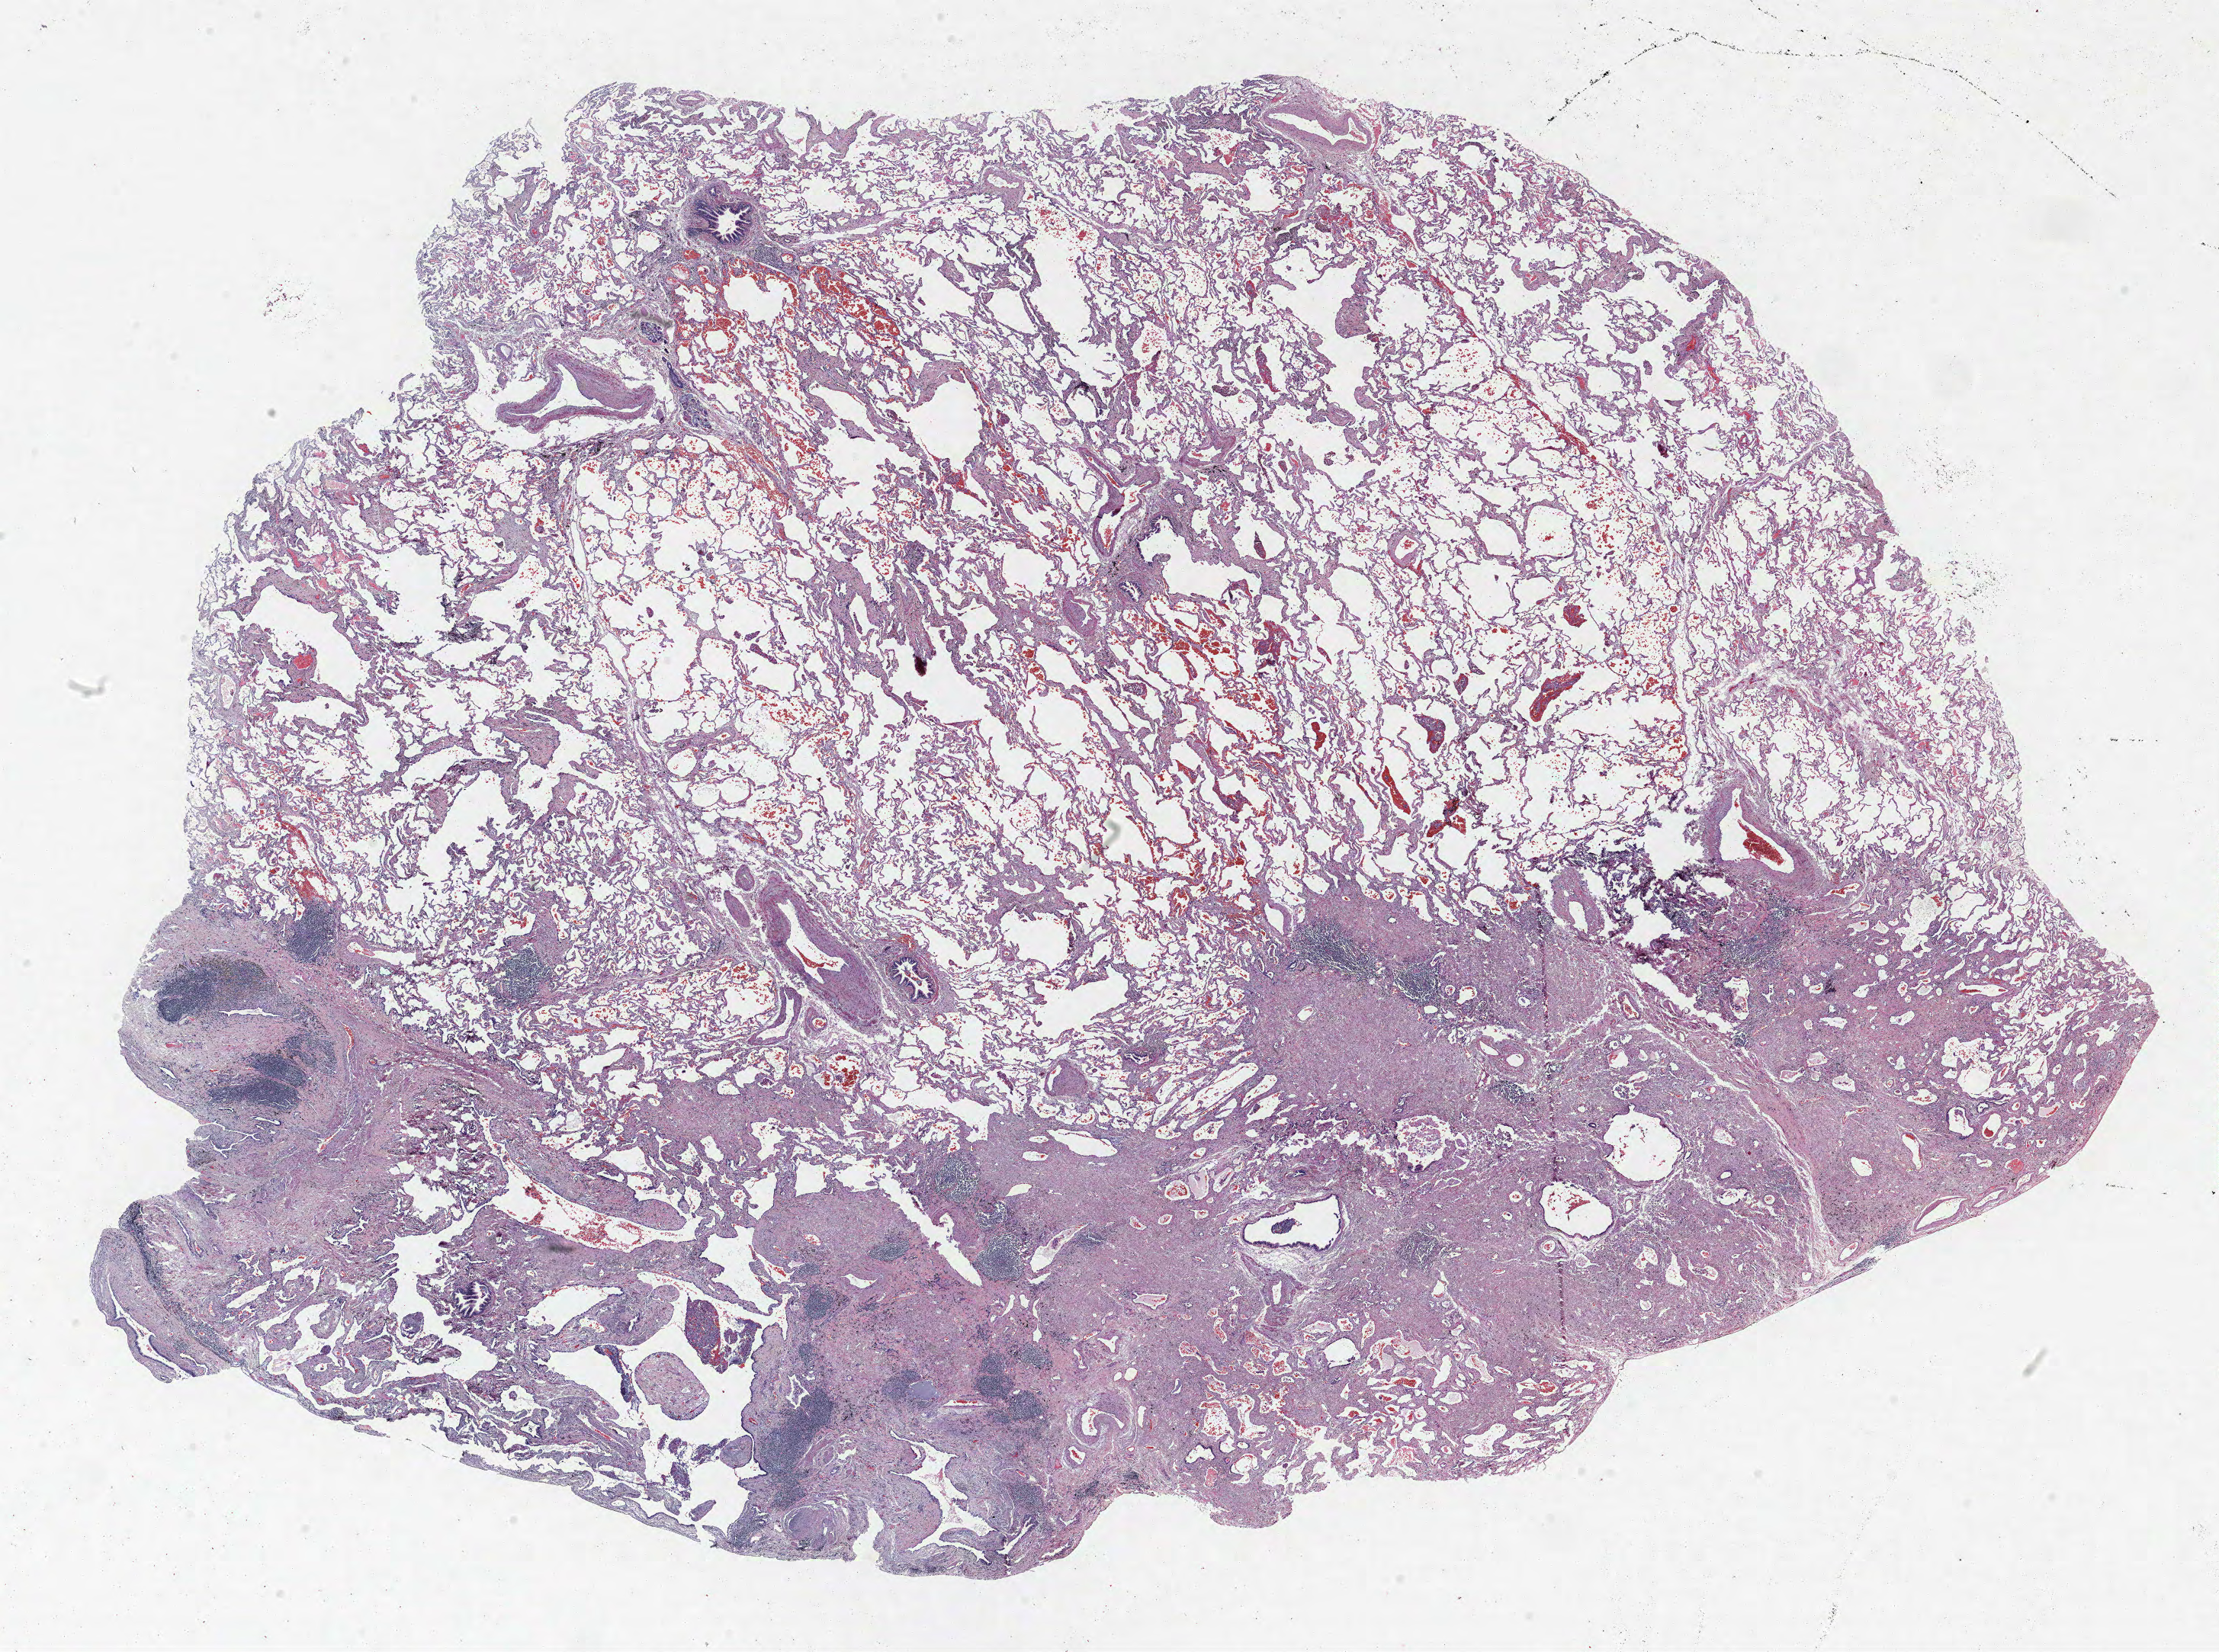
Whole-slide histology image, H&E, whole scanned area (about 23.3 x 17.3 mm) shown as a low-resolution overview; formalin-fixed paraffin-embedded (FFPE) section; lung tissue. Female, age 66 at enrolment. Current smoker at enrolment. Grade: poorly differentiated (G3).
* participant's lung-cancer diagnosis: Adenocarcinoma, NOS (ICD-O-3 8140/3)
* tumour size (pathology): 18 mm
* stage (AJCC 6th edition): IA
* primary tumour location (clinical record): right upper lobe